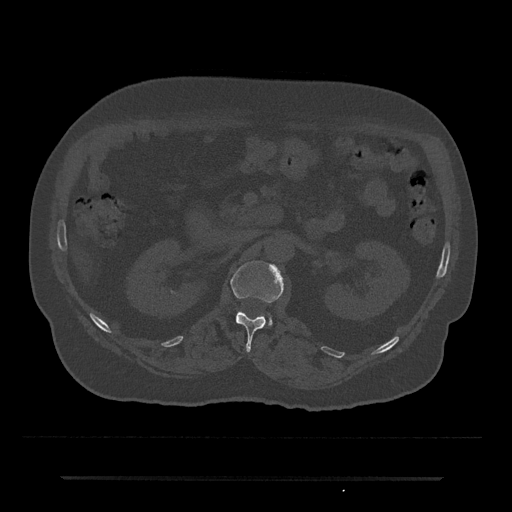
CT including the spine, one axial slice; position 59 of 797 along the scan axis; reconstruction kernel Br40s/3; 120 kVp; bone window (W 1800 / L 400 HU); 512 × 512 image matrix, field of view 437 × 437 mm. Patient: male, 69 years. Case-level facts recorded for this patient, not image findings: primary cancer: prostate.
Structures marked on this image (semi-automatically segmented with operator editing):
- L1 vertebra: bounding box <231,261,283,350> (left, top, right, bottom; pixels)
- L2 vertebra: <270,319,272,325>